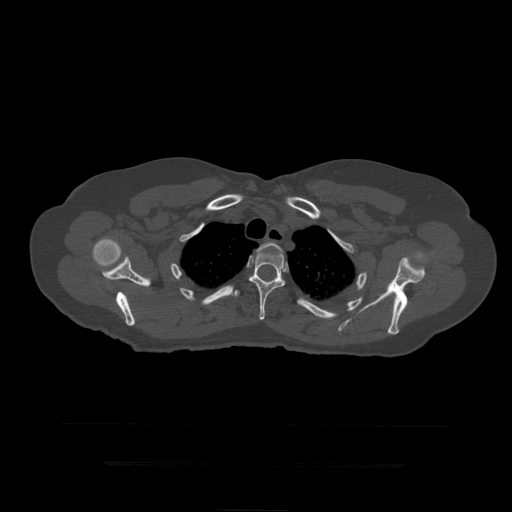
CT including the spine, one axial slice. Position 350 of 399 along the scan axis. Reconstruction kernel STANDARD. 120 kVp. Bone window (W 1800 / L 400 HU). 512 × 512 image matrix, field of view 450 × 450 mm. Patient age 41 years. From the clinical record (not read from this slice): primary cancer: breast.
Outlined on this slice (semi-automatic segmentation, software-assisted and operator-edited):
- T3 vertebra: bounding box (x1, y1, x2, y2) in pixels: (253, 242, 283, 257)
- T4 vertebra: (249, 251, 286, 320)
- T5 vertebra: (235, 291, 240, 297)